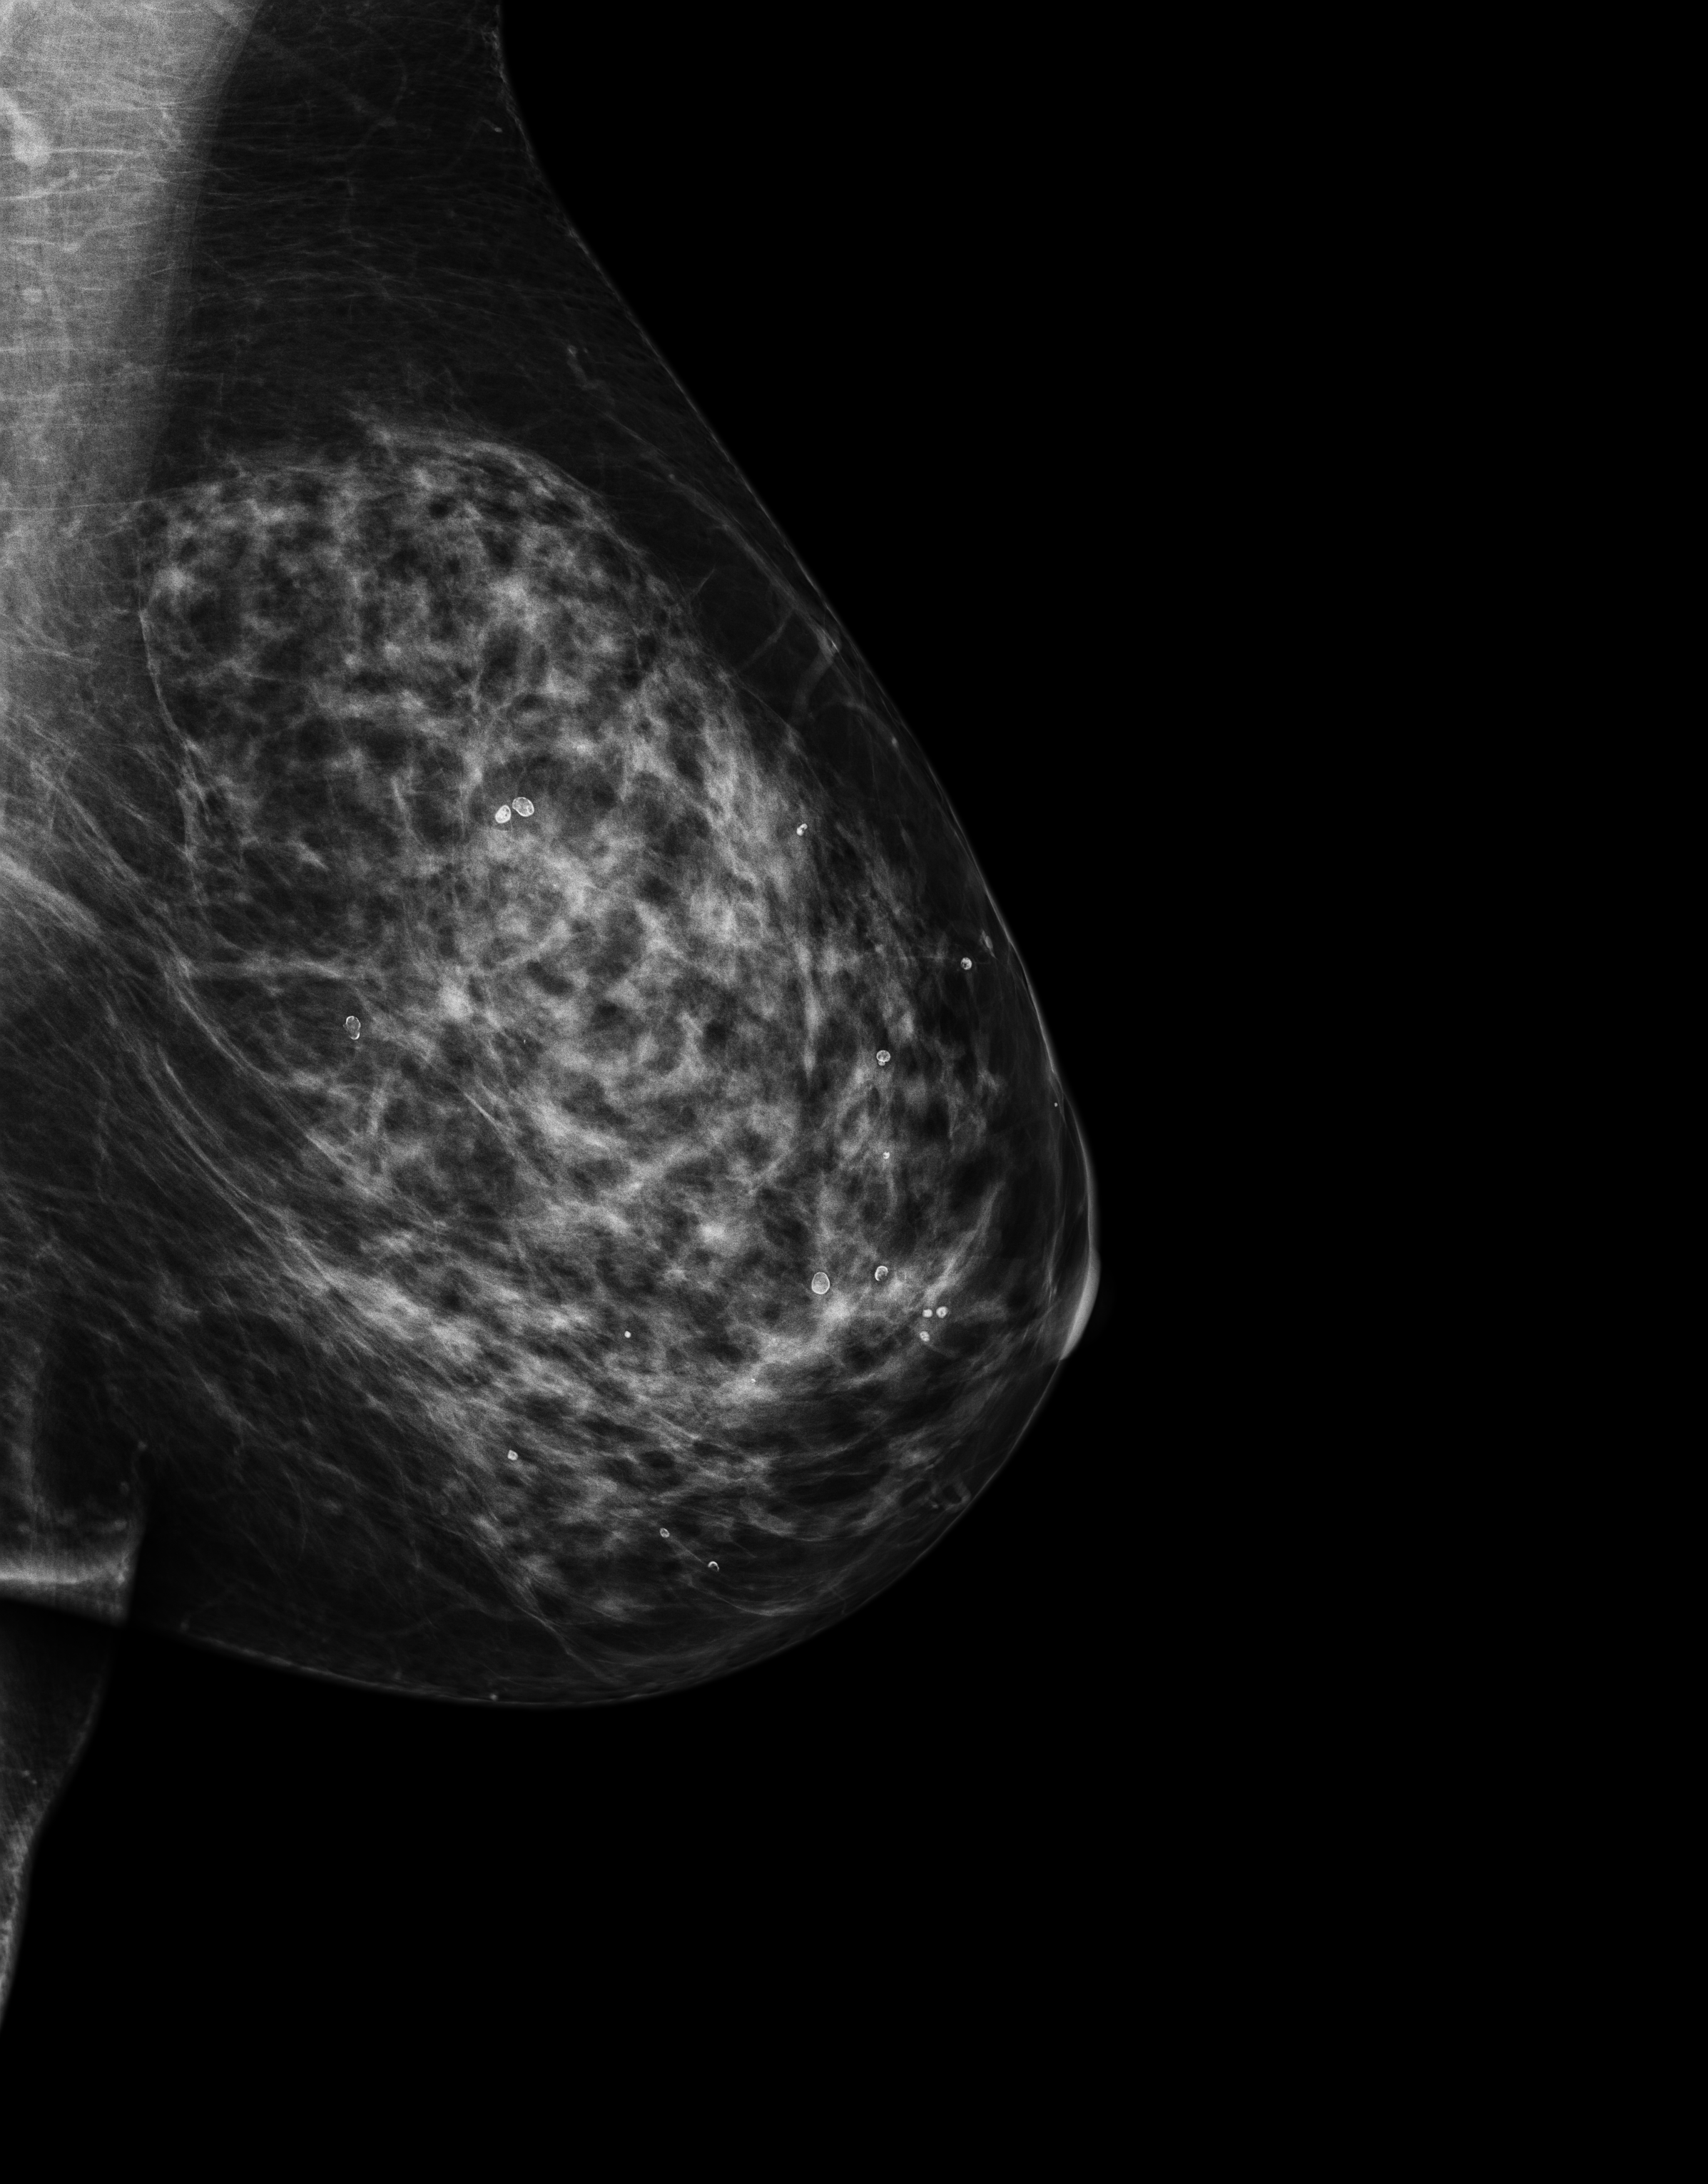
Full-field digital mammogram (FFDM), left breast, mediolateral oblique (MLO) view, annual screening mammography examination, compressed breast thickness 70 mm, system: Senographe Essential ADS_56.21.3. Patient aged 66 years (female).
Breast density at the screening exam (both breasts): heterogeneously dense (BI-RADS density category c). Final BI-RADS assessment for this screening round (tomosynthesis exam, both breasts): category 1. Recall: no recall after this screen.